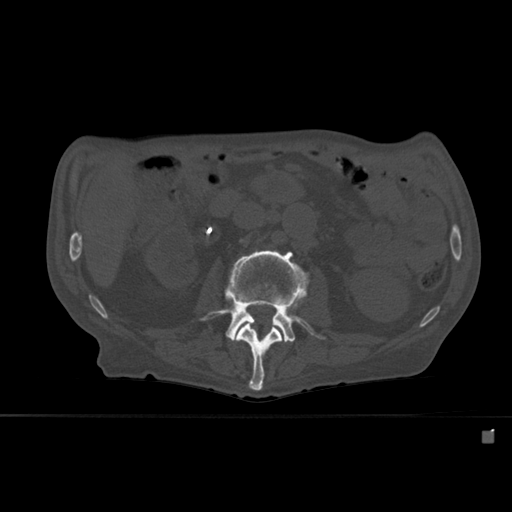
CT including the spine, one axial slice; position 222 of 527 along the scan axis; bone window (W 1800 / L 400 HU); 1.5 mm slice thickness; 512 × 512 image matrix, field of view 373 × 373 mm. Male patient, age 78 years. From the clinical record (not read from this slice): primary cancer: prostate.
Structures marked on this image (semi-automatic segmentation, software-assisted and operator-edited):
- L2 vertebra: bounding box <225,294,282,391> (left, top, right, bottom; pixels)
- L3 vertebra: <202,250,322,342>